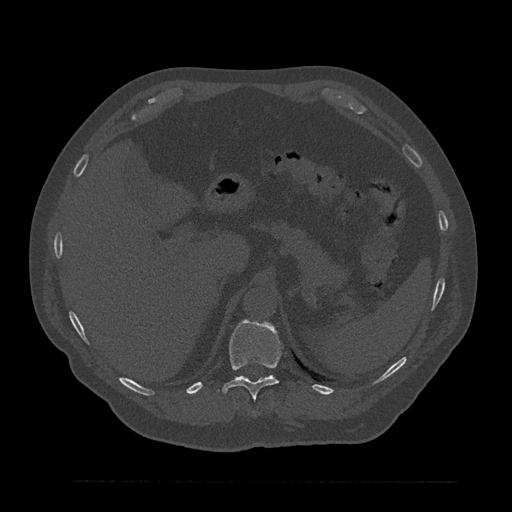
CT including the spine, one axial slice; slice 287 of 797 in the series (ordered by position); bone window (W 1800 / L 400 HU); 0.5 mm slice thickness; 512 × 512 image matrix, field of view 430 × 430 mm. Male patient, age 61 years. From the clinical record (not read from this slice): primary cancer: prostate.
Outlined on this slice (semi-automatic segmentation, software-assisted and operator-edited):
- T11 vertebra: bounding box [x1, y1, x2, y2] px = [218, 320, 281, 400]